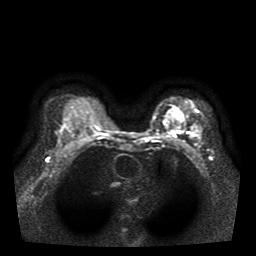
Breast MRI, one axial slice. Position 27 of 39 along the scan axis. Diffusion-weighted series; image 2 of 4 stored at this slice position (different b-values; order by instance number). 1.5 T. 256 × 256 image matrix. Female patient.
Structures marked on this image (expert manual segmentation):
- tumour on diffusion-weighted imaging: bounding box (x1, y1, x2, y2) in pixels: (177, 111, 183, 119)